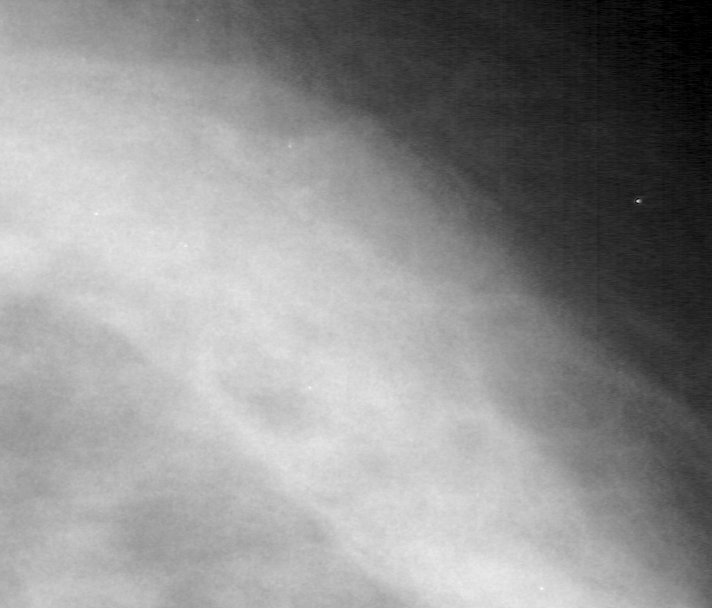
Region of interest cut from a scanned film mammogram (one marked finding); right breast; MLO view.
- Mass, shape asymmetric breast tissue, margins obscured; BI-RADS assessment category 4; benign without callback (not worked up further).